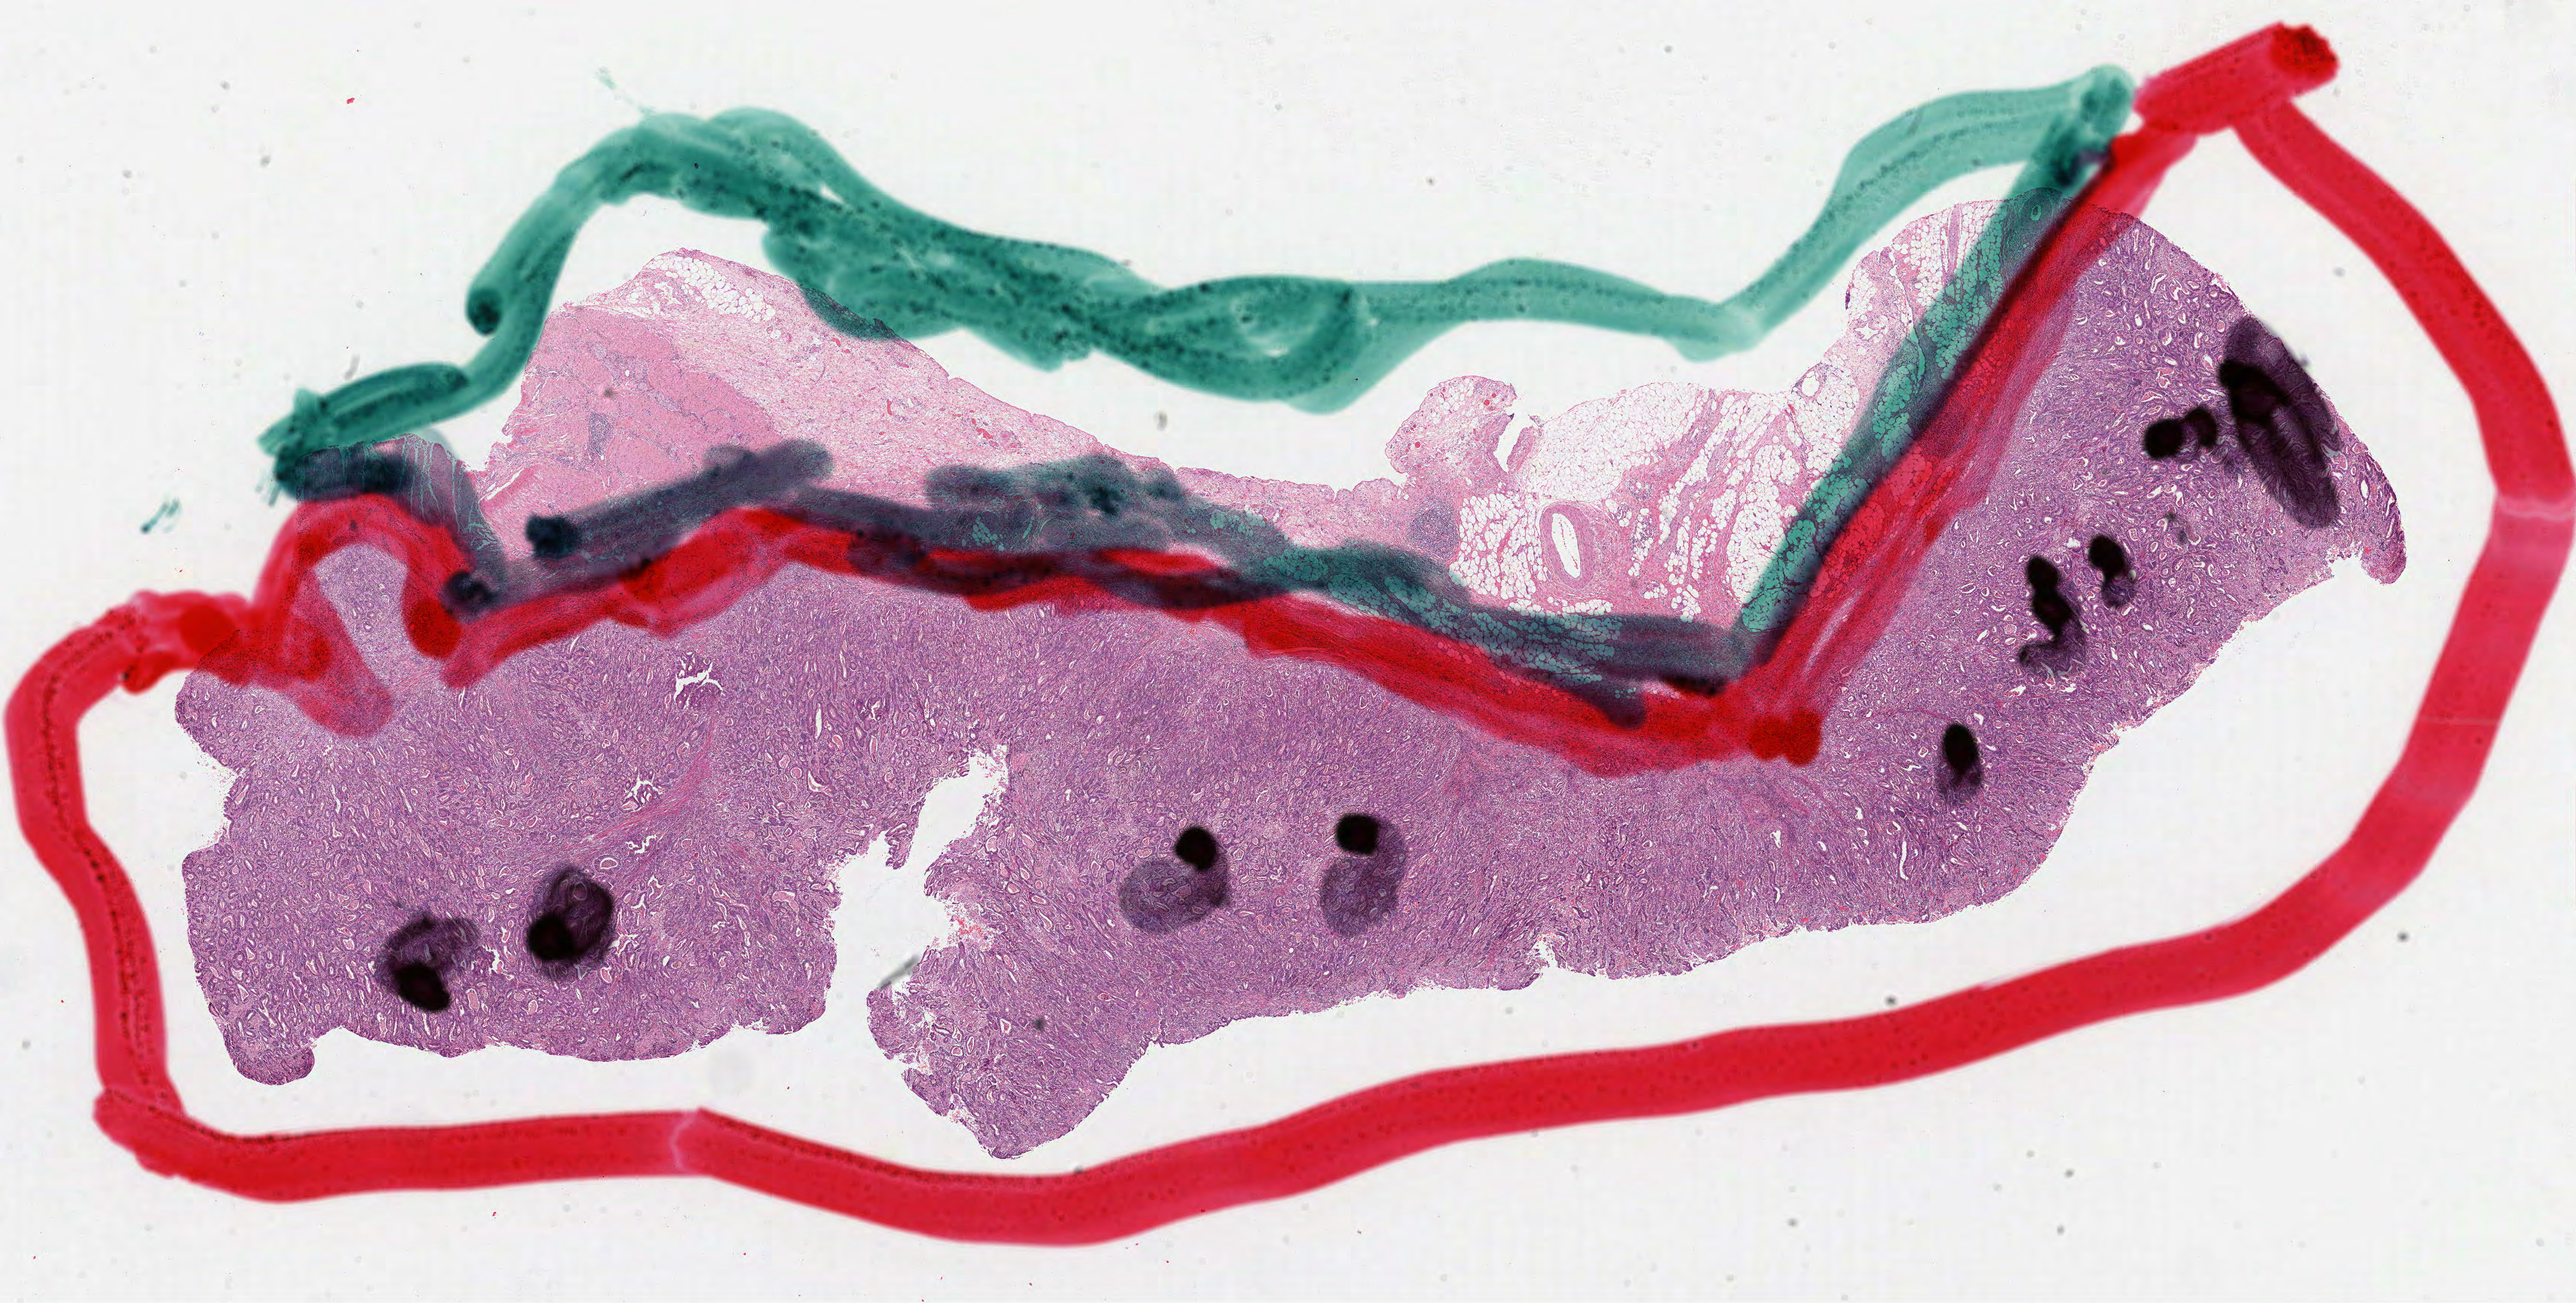
Whole-slide histology image, H&E-stained — low-resolution overview of the scanned area, about 27.6 x 13.9 mm (from a 40x scan), formalin-fixed paraffin-embedded (FFPE) diagnostic section, primary tumour sample from the stomach. Female, age 71 years at initial diagnosis. Histologic grade: G2 (moderately differentiated).
- AJCC pathologic stage: IIB
- histologic diagnosis: Adenocarcinoma, NOS (body of stomach)